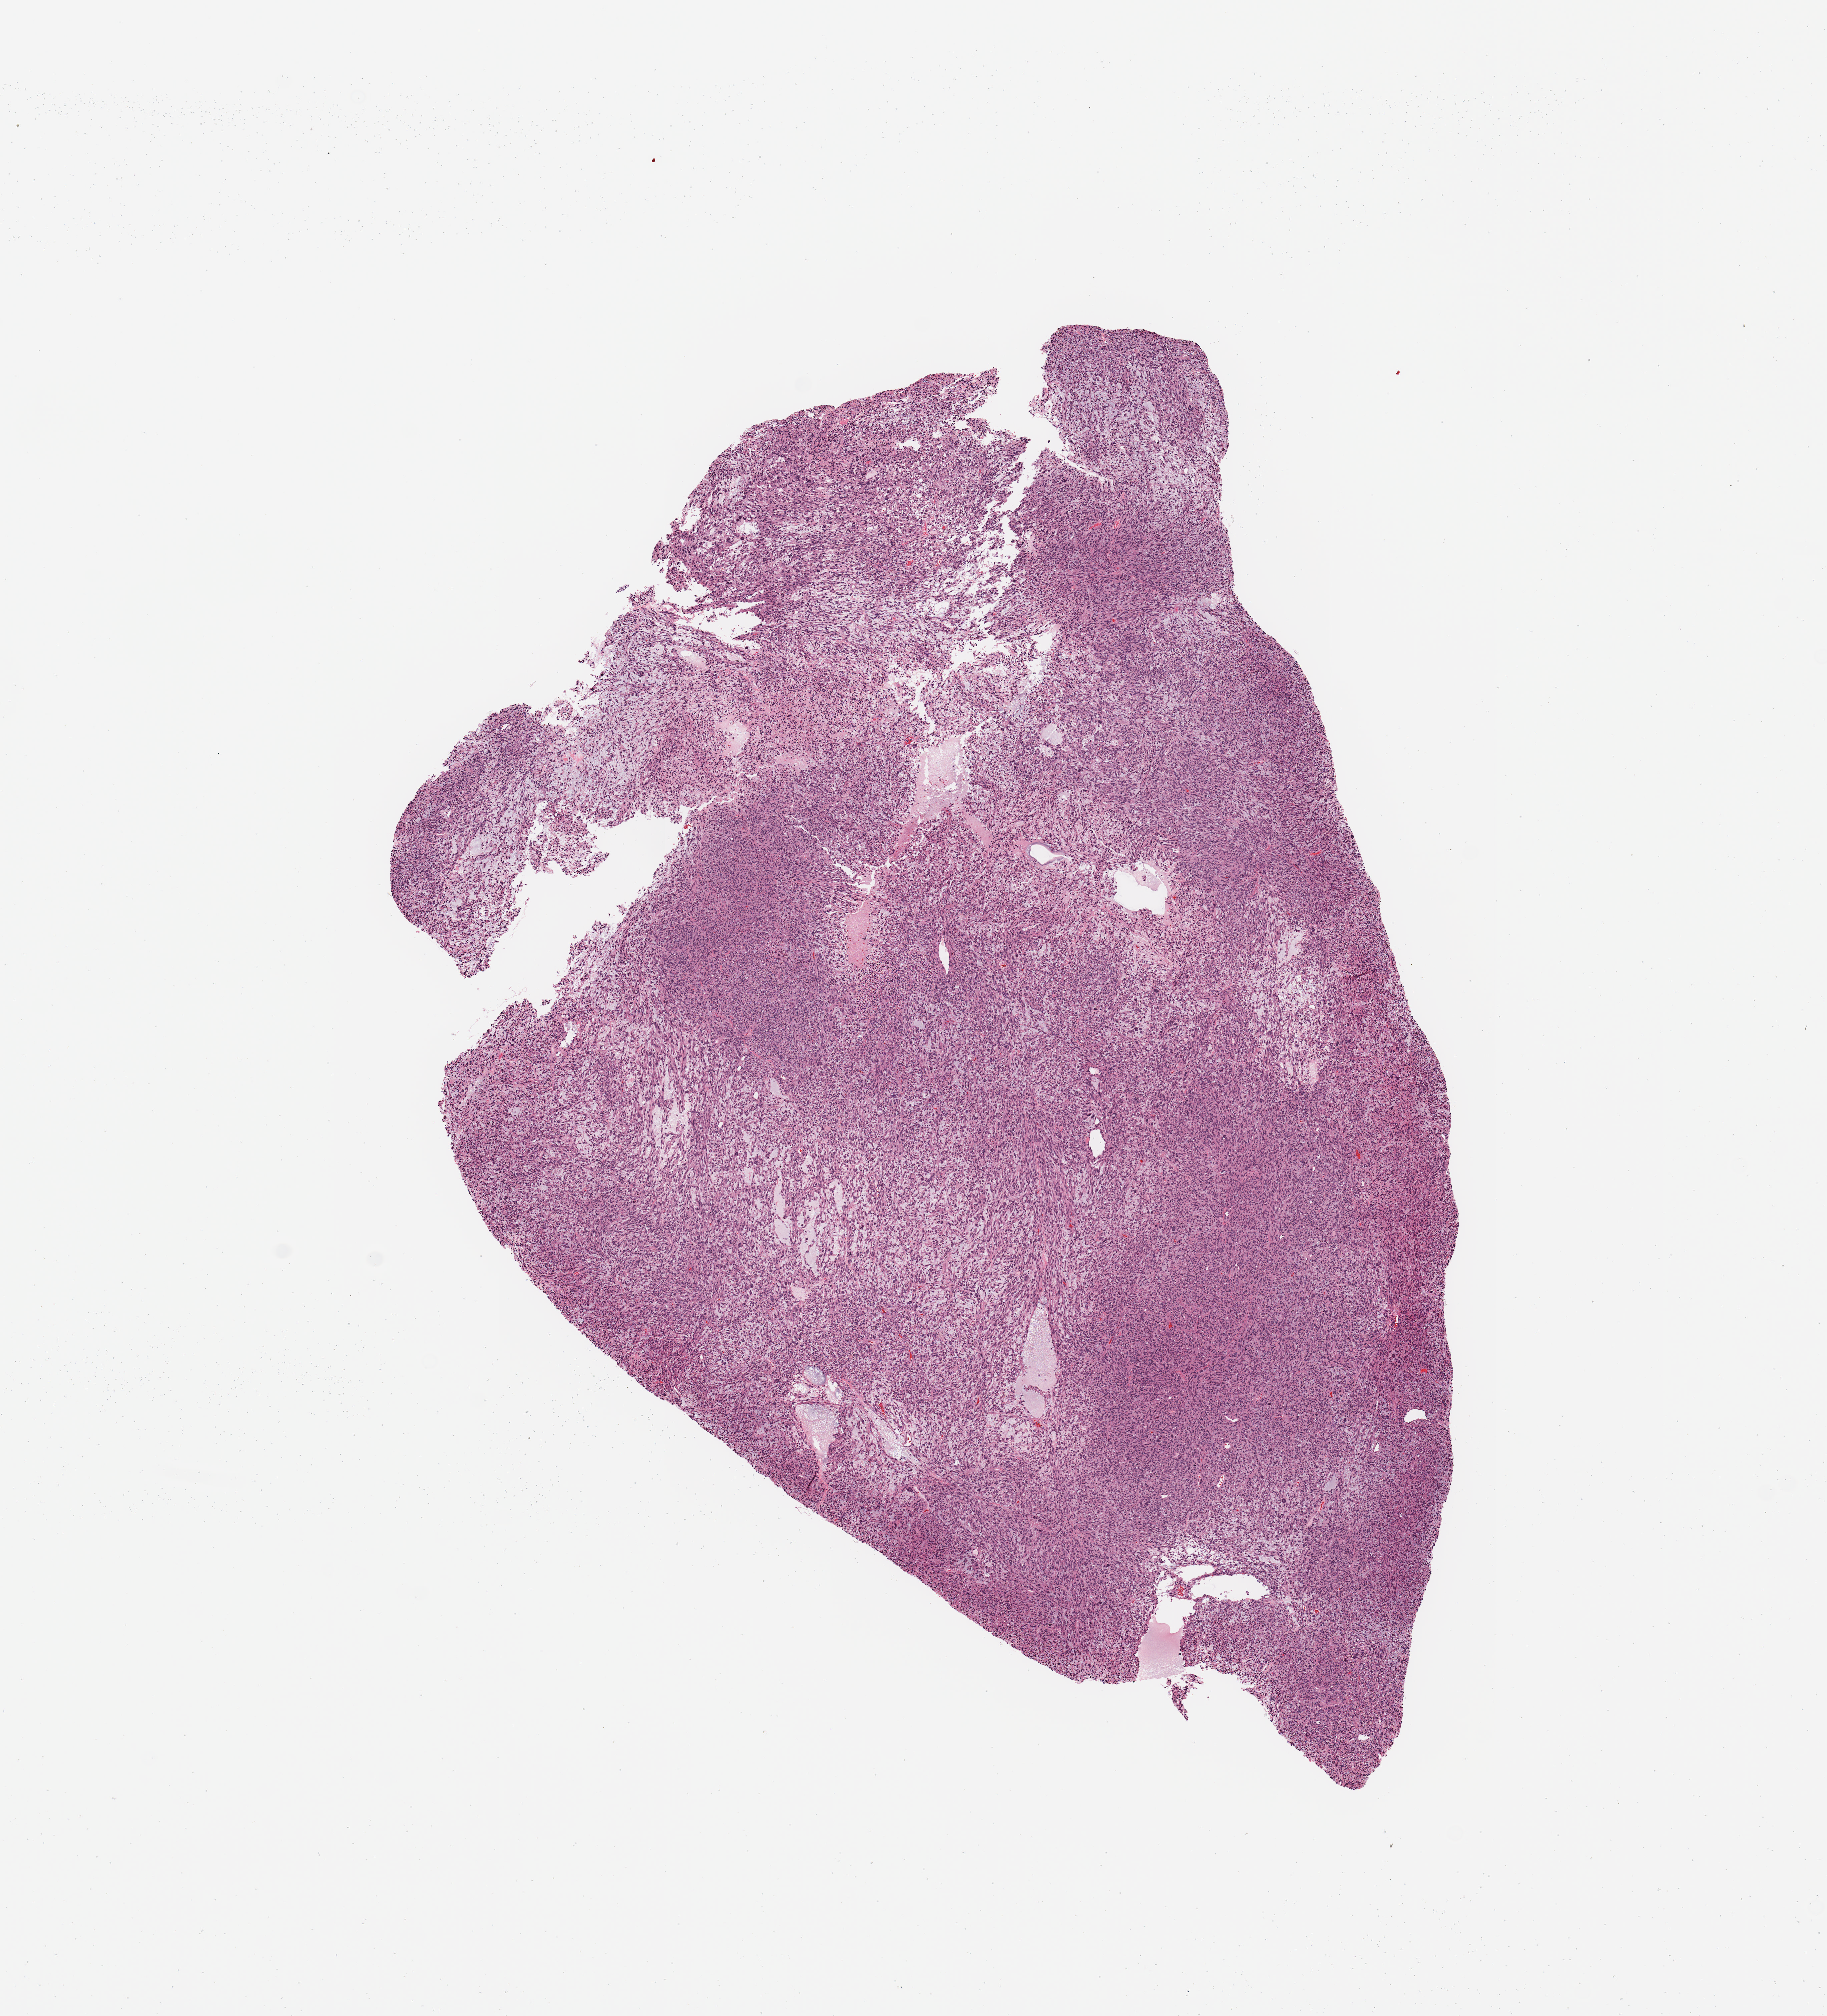
H&E-stained whole-slide image, whole scanned area (about 10.8 x 11.9 mm) shown as a low-resolution overview. Male, 68 y/o.
* patient diagnosis (cohort enrolment): sarcoma (site not recorded at cohort level)